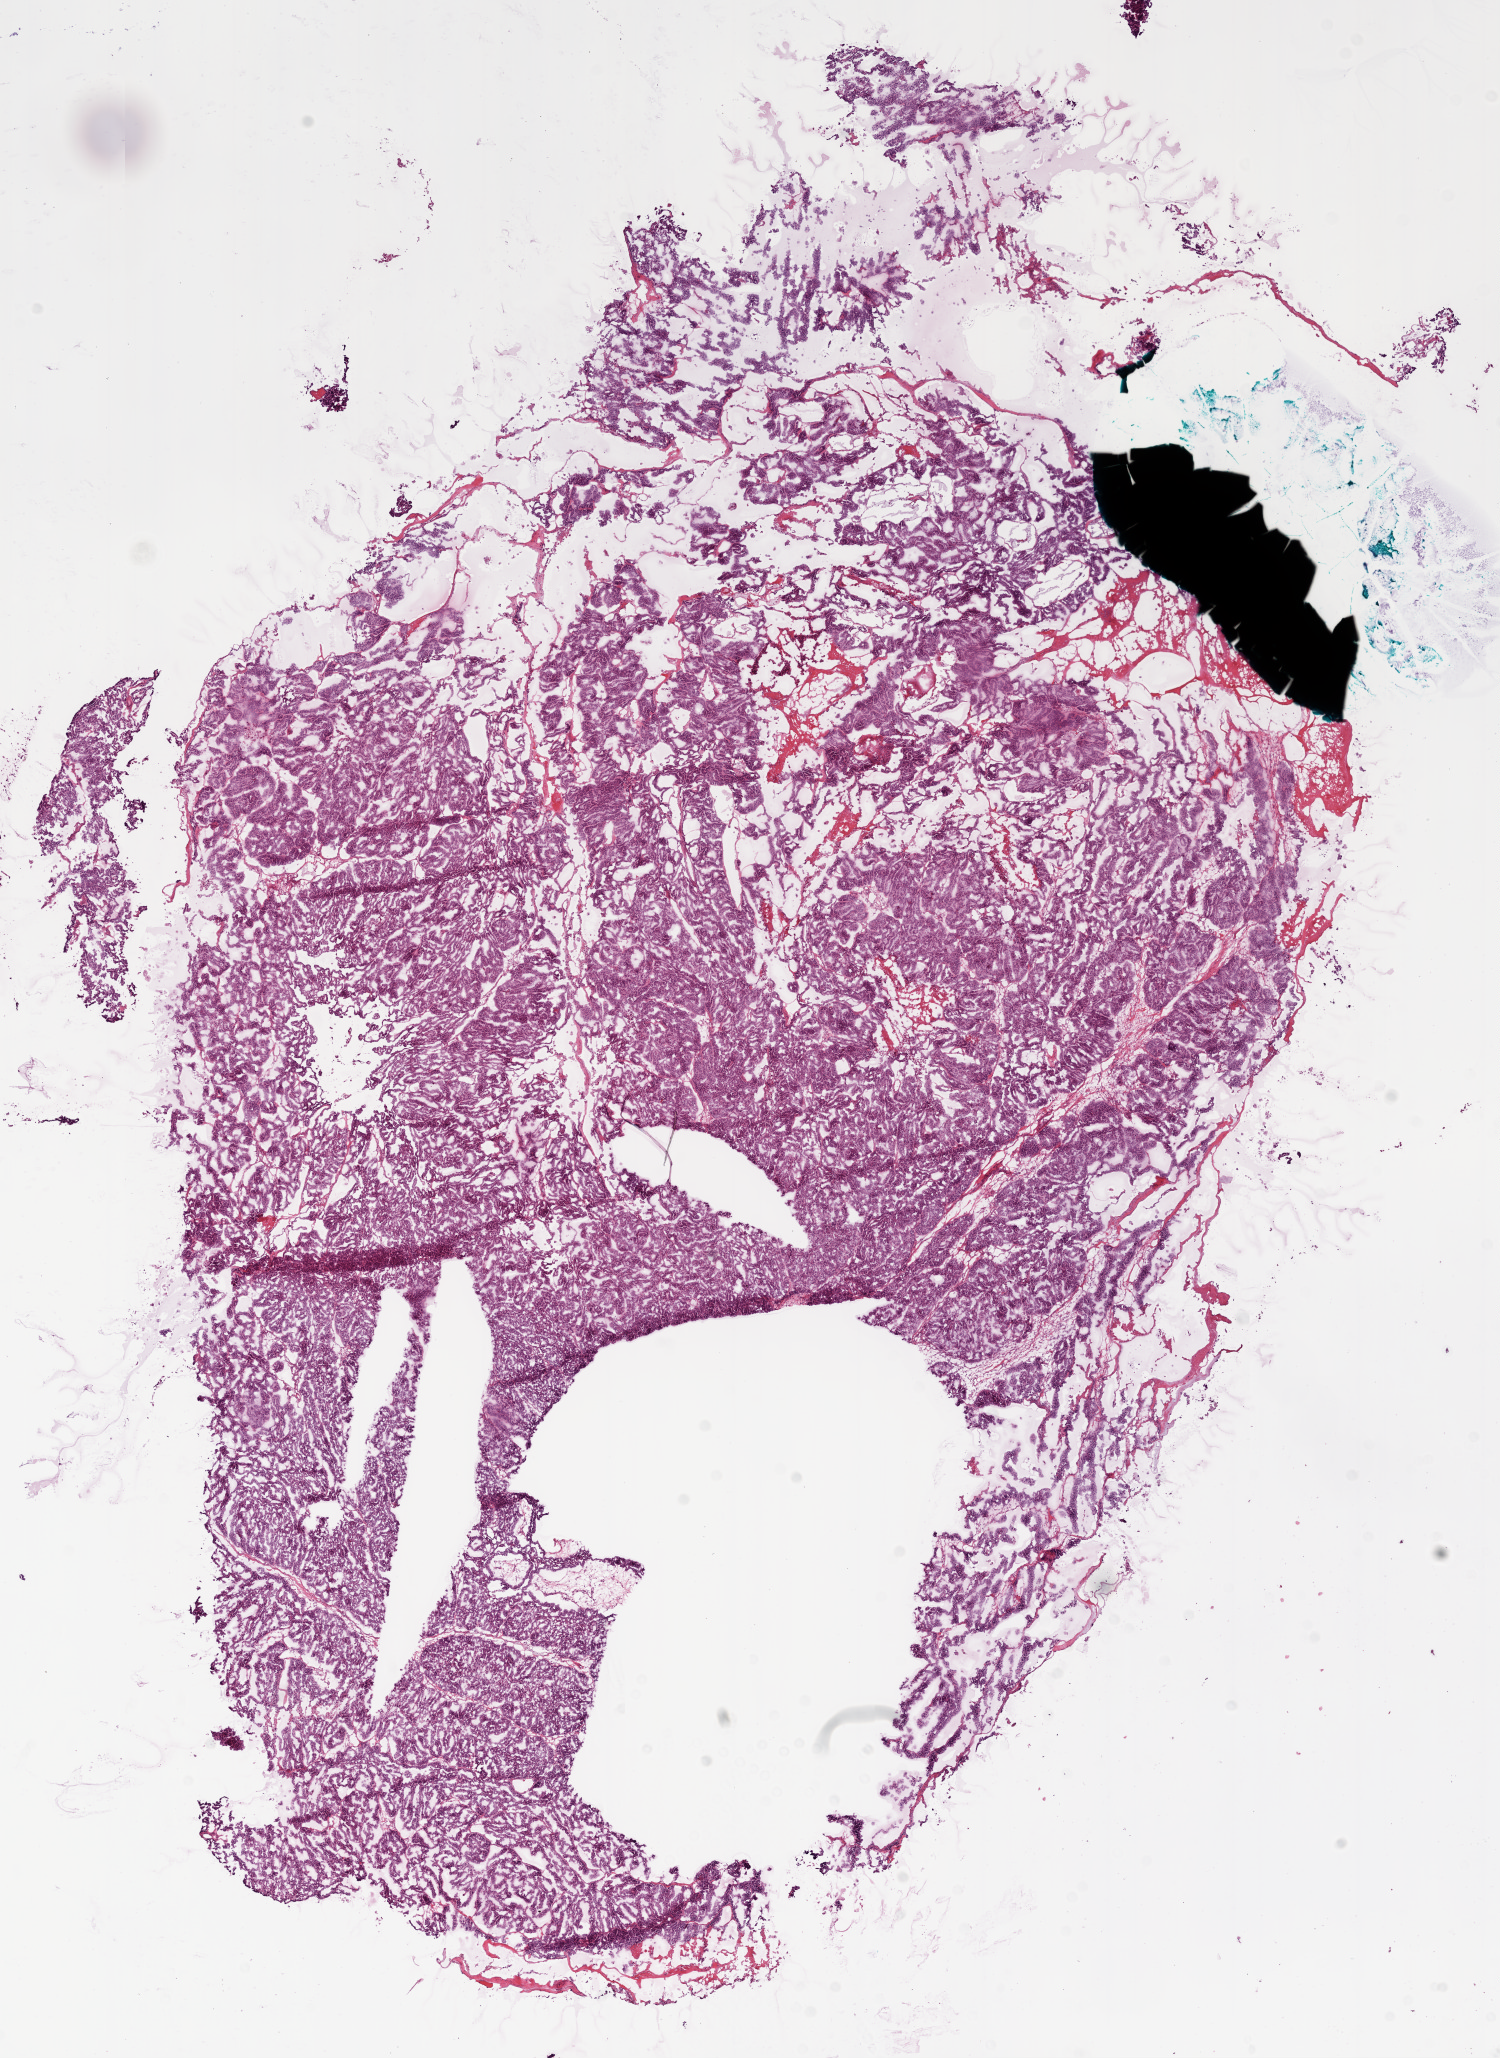
H&E-stained whole-slide image, whole scanned area (about 12.0 x 16.5 mm) shown as a low-resolution overview; frozen section from the bottom of the tissue portion; primary tumour sample from the ovary. Patient: female, age at initial diagnosis 51 years. Histologic grade: G3 (poorly differentiated). Pathologist review of this section (percent, as recorded): tumour cells 95%, tumour nuclei 95%, normal cells 0%, stromal cells 5%, necrosis 0%.
• FIGO stage: IIIC
• pathologic diagnosis: Serous cystadenocarcinoma, NOS